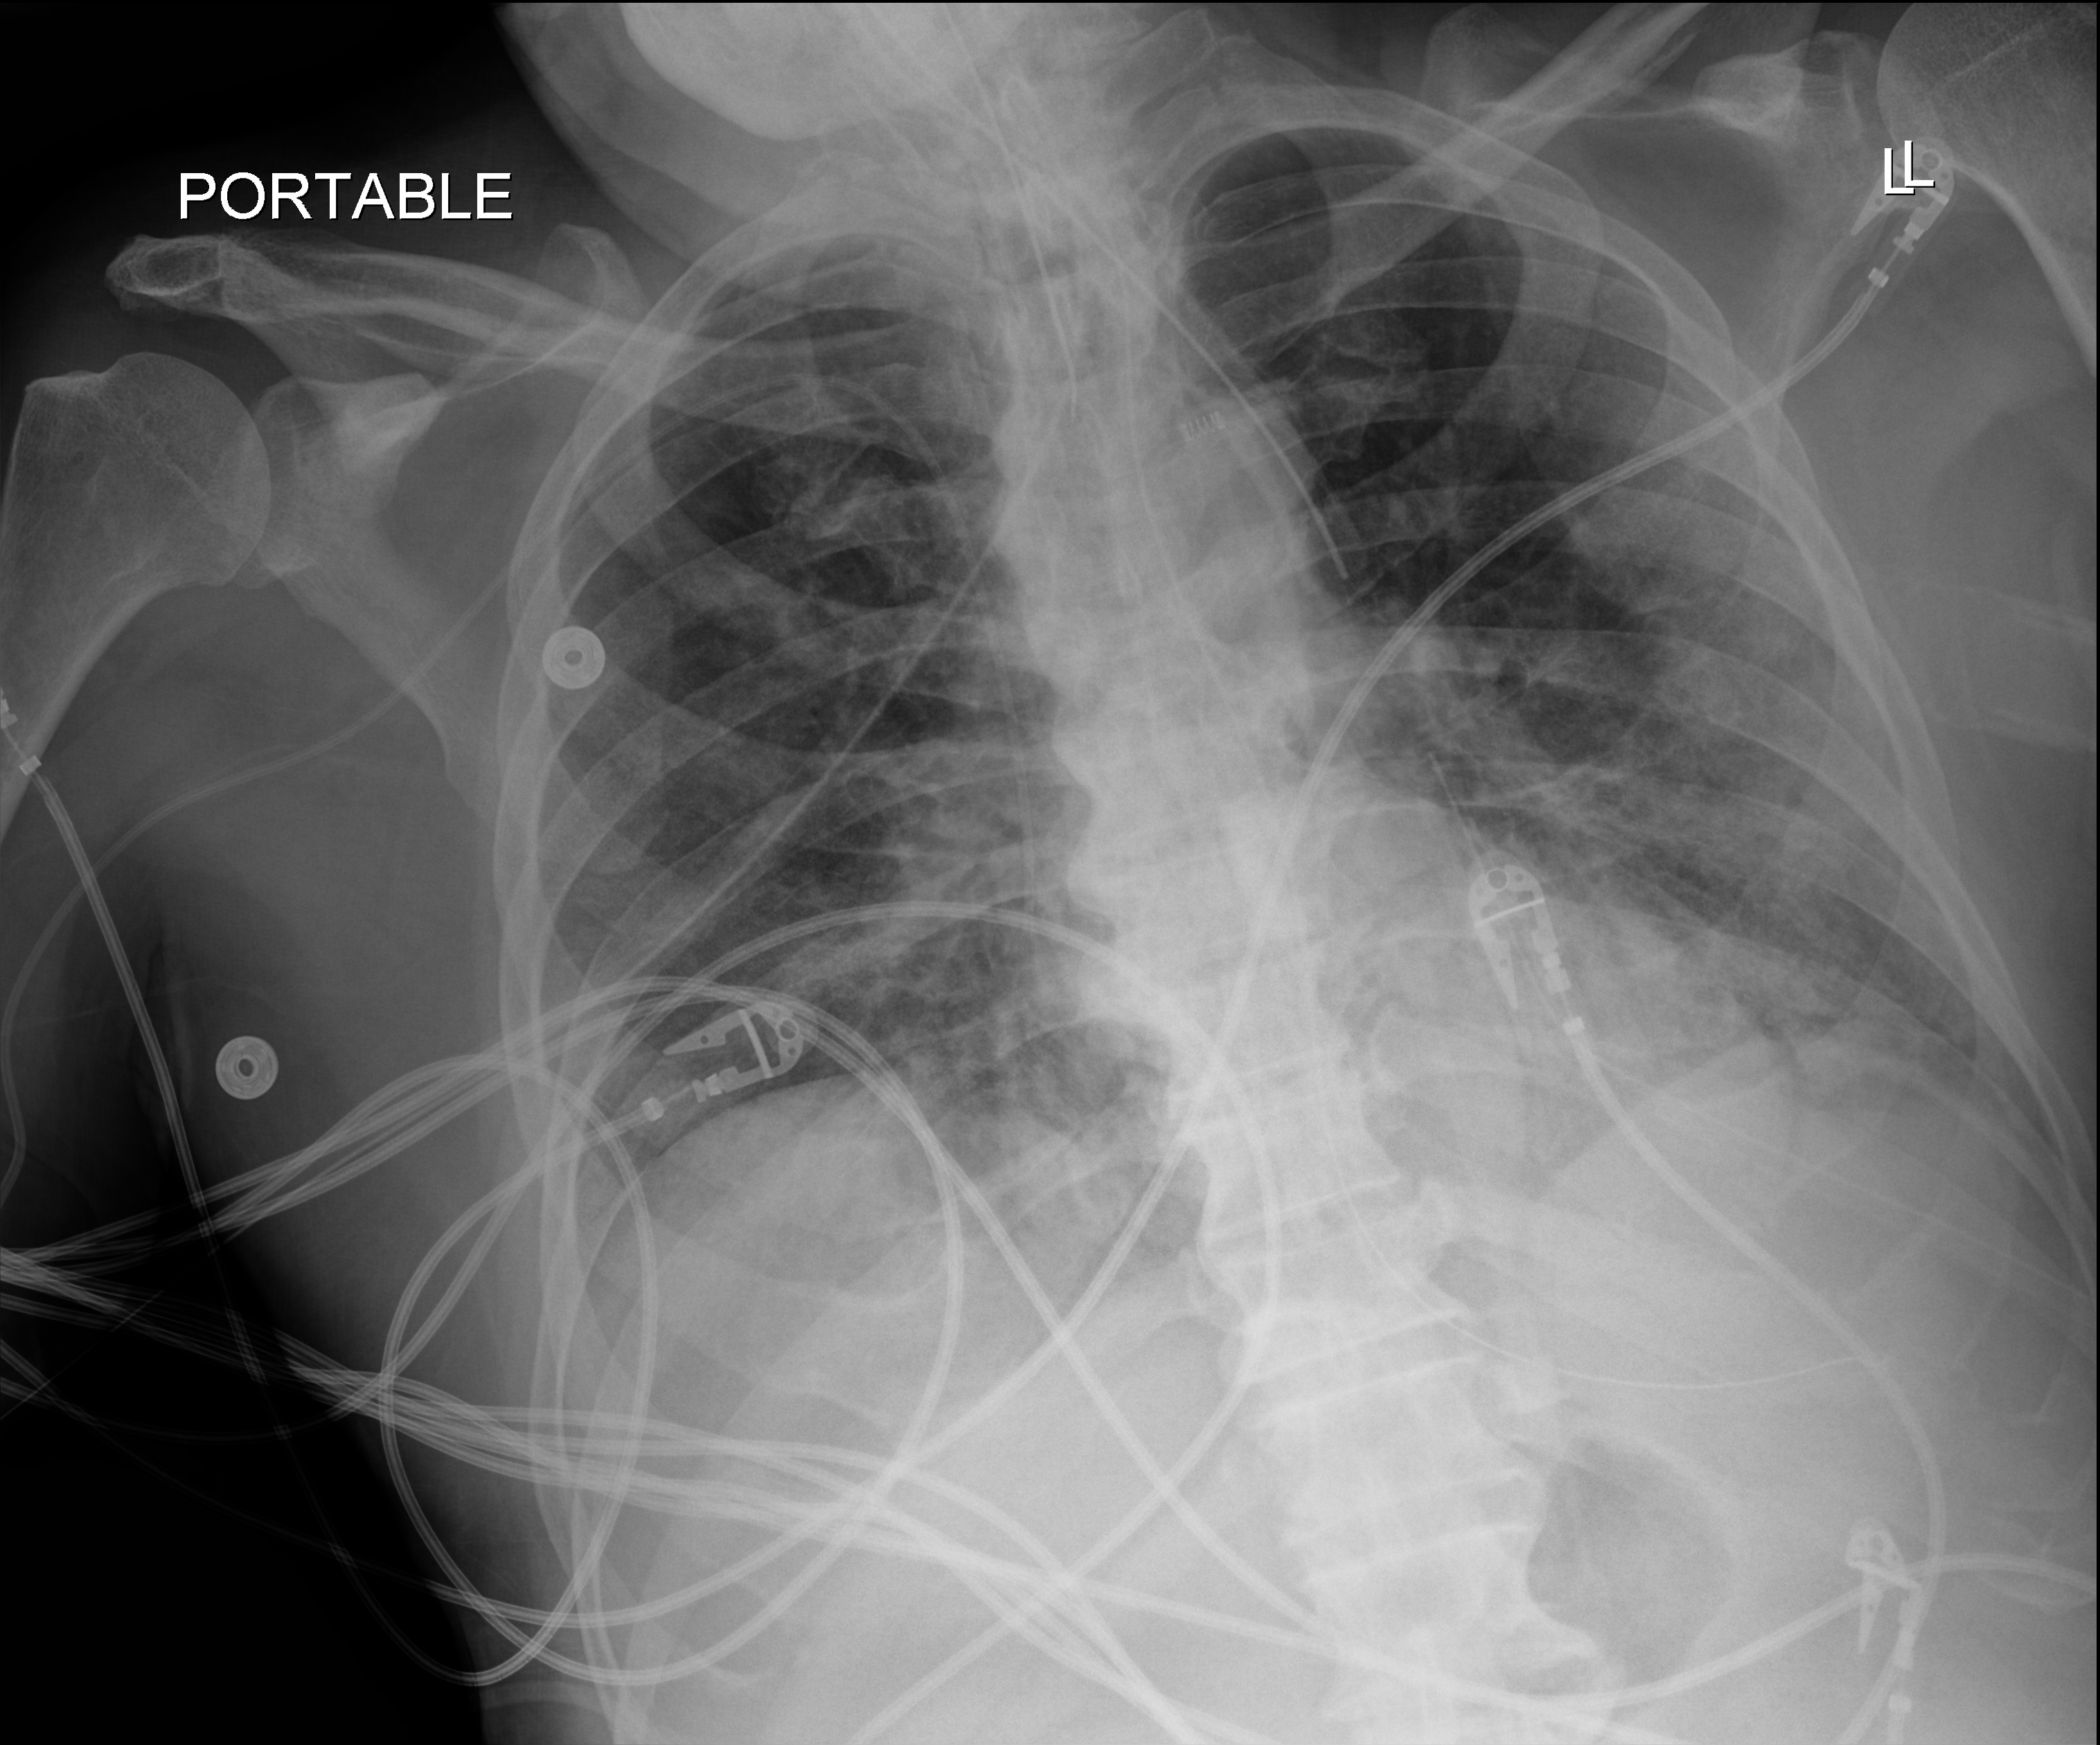
Chest X-ray (portable), anteroposterior (AP) projection. Male patient hospitalised with COVID-19, age 75–90 years.
Admission-level facts for this patient (not findings on this image; timing relative to this image not recorded): COPD (admission record): no; length of hospital stay: 33 days; other chronic lung disease (admission record): no.